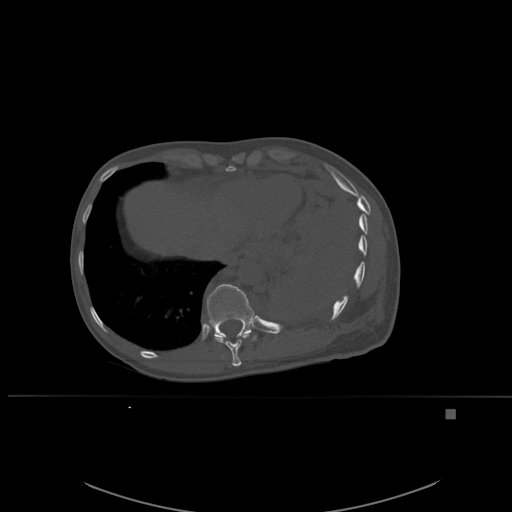
CT including the spine, one axial slice; slice 308 of 537 in the series (ordered by position); bone window (W 1800 / L 400 HU); 512 × 512 image matrix, field of view 440 × 440 mm. Patient: female, 45 years. Case-level facts recorded for this patient, not image findings: primary cancer: lung.
Outlined on this slice (semi-automatic segmentation, software-assisted and operator-edited):
- T10 vertebra: bounding box [x1, y1, x2, y2] px = [214, 333, 256, 366]
- T11 vertebra: [207, 284, 257, 339]